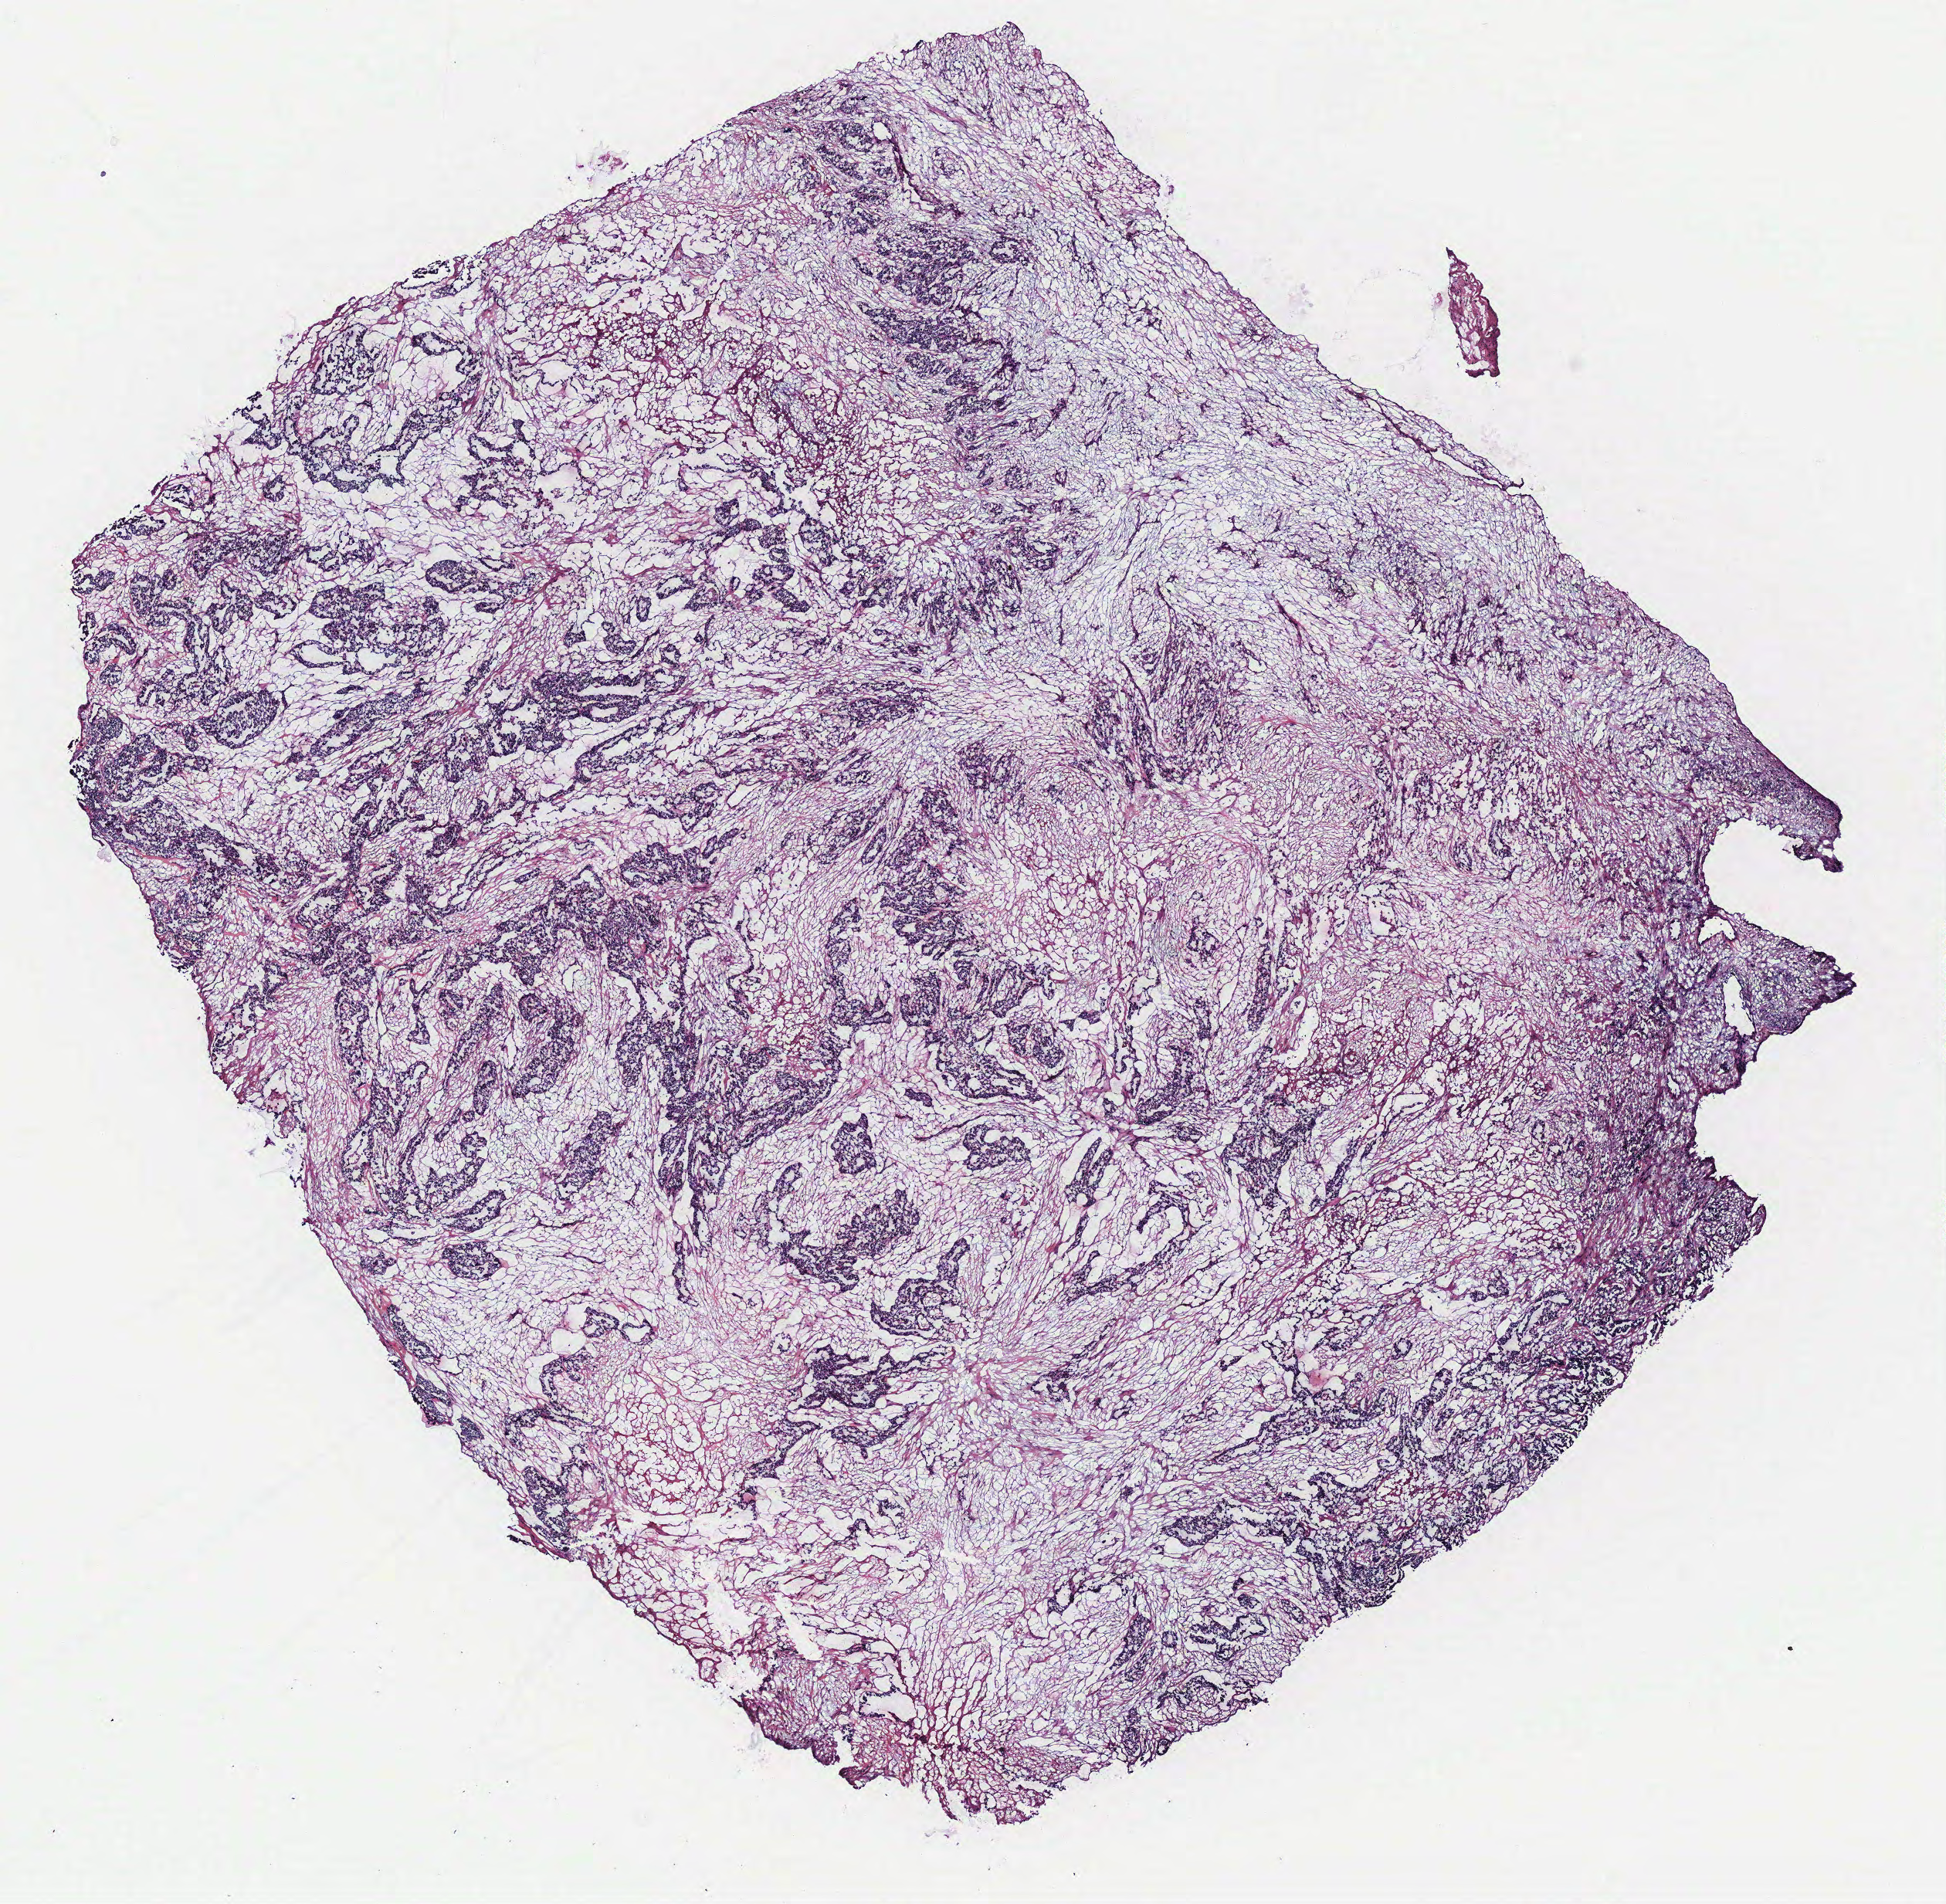
Whole-slide histology image, Hematoxylin and eosin (H&E) stained — shown as a low-resolution overview of the whole scanned area (about 10.1 x 9.9 mm, from a 40x scan); ovary, normal (non-tumour) tissue. Patient: female, age 58 years.
• this section: normal (non-tumour) tissue from the same patient
• patient diagnosis: Serous adenocarcinoma, NOS (peritoneum, NOS)